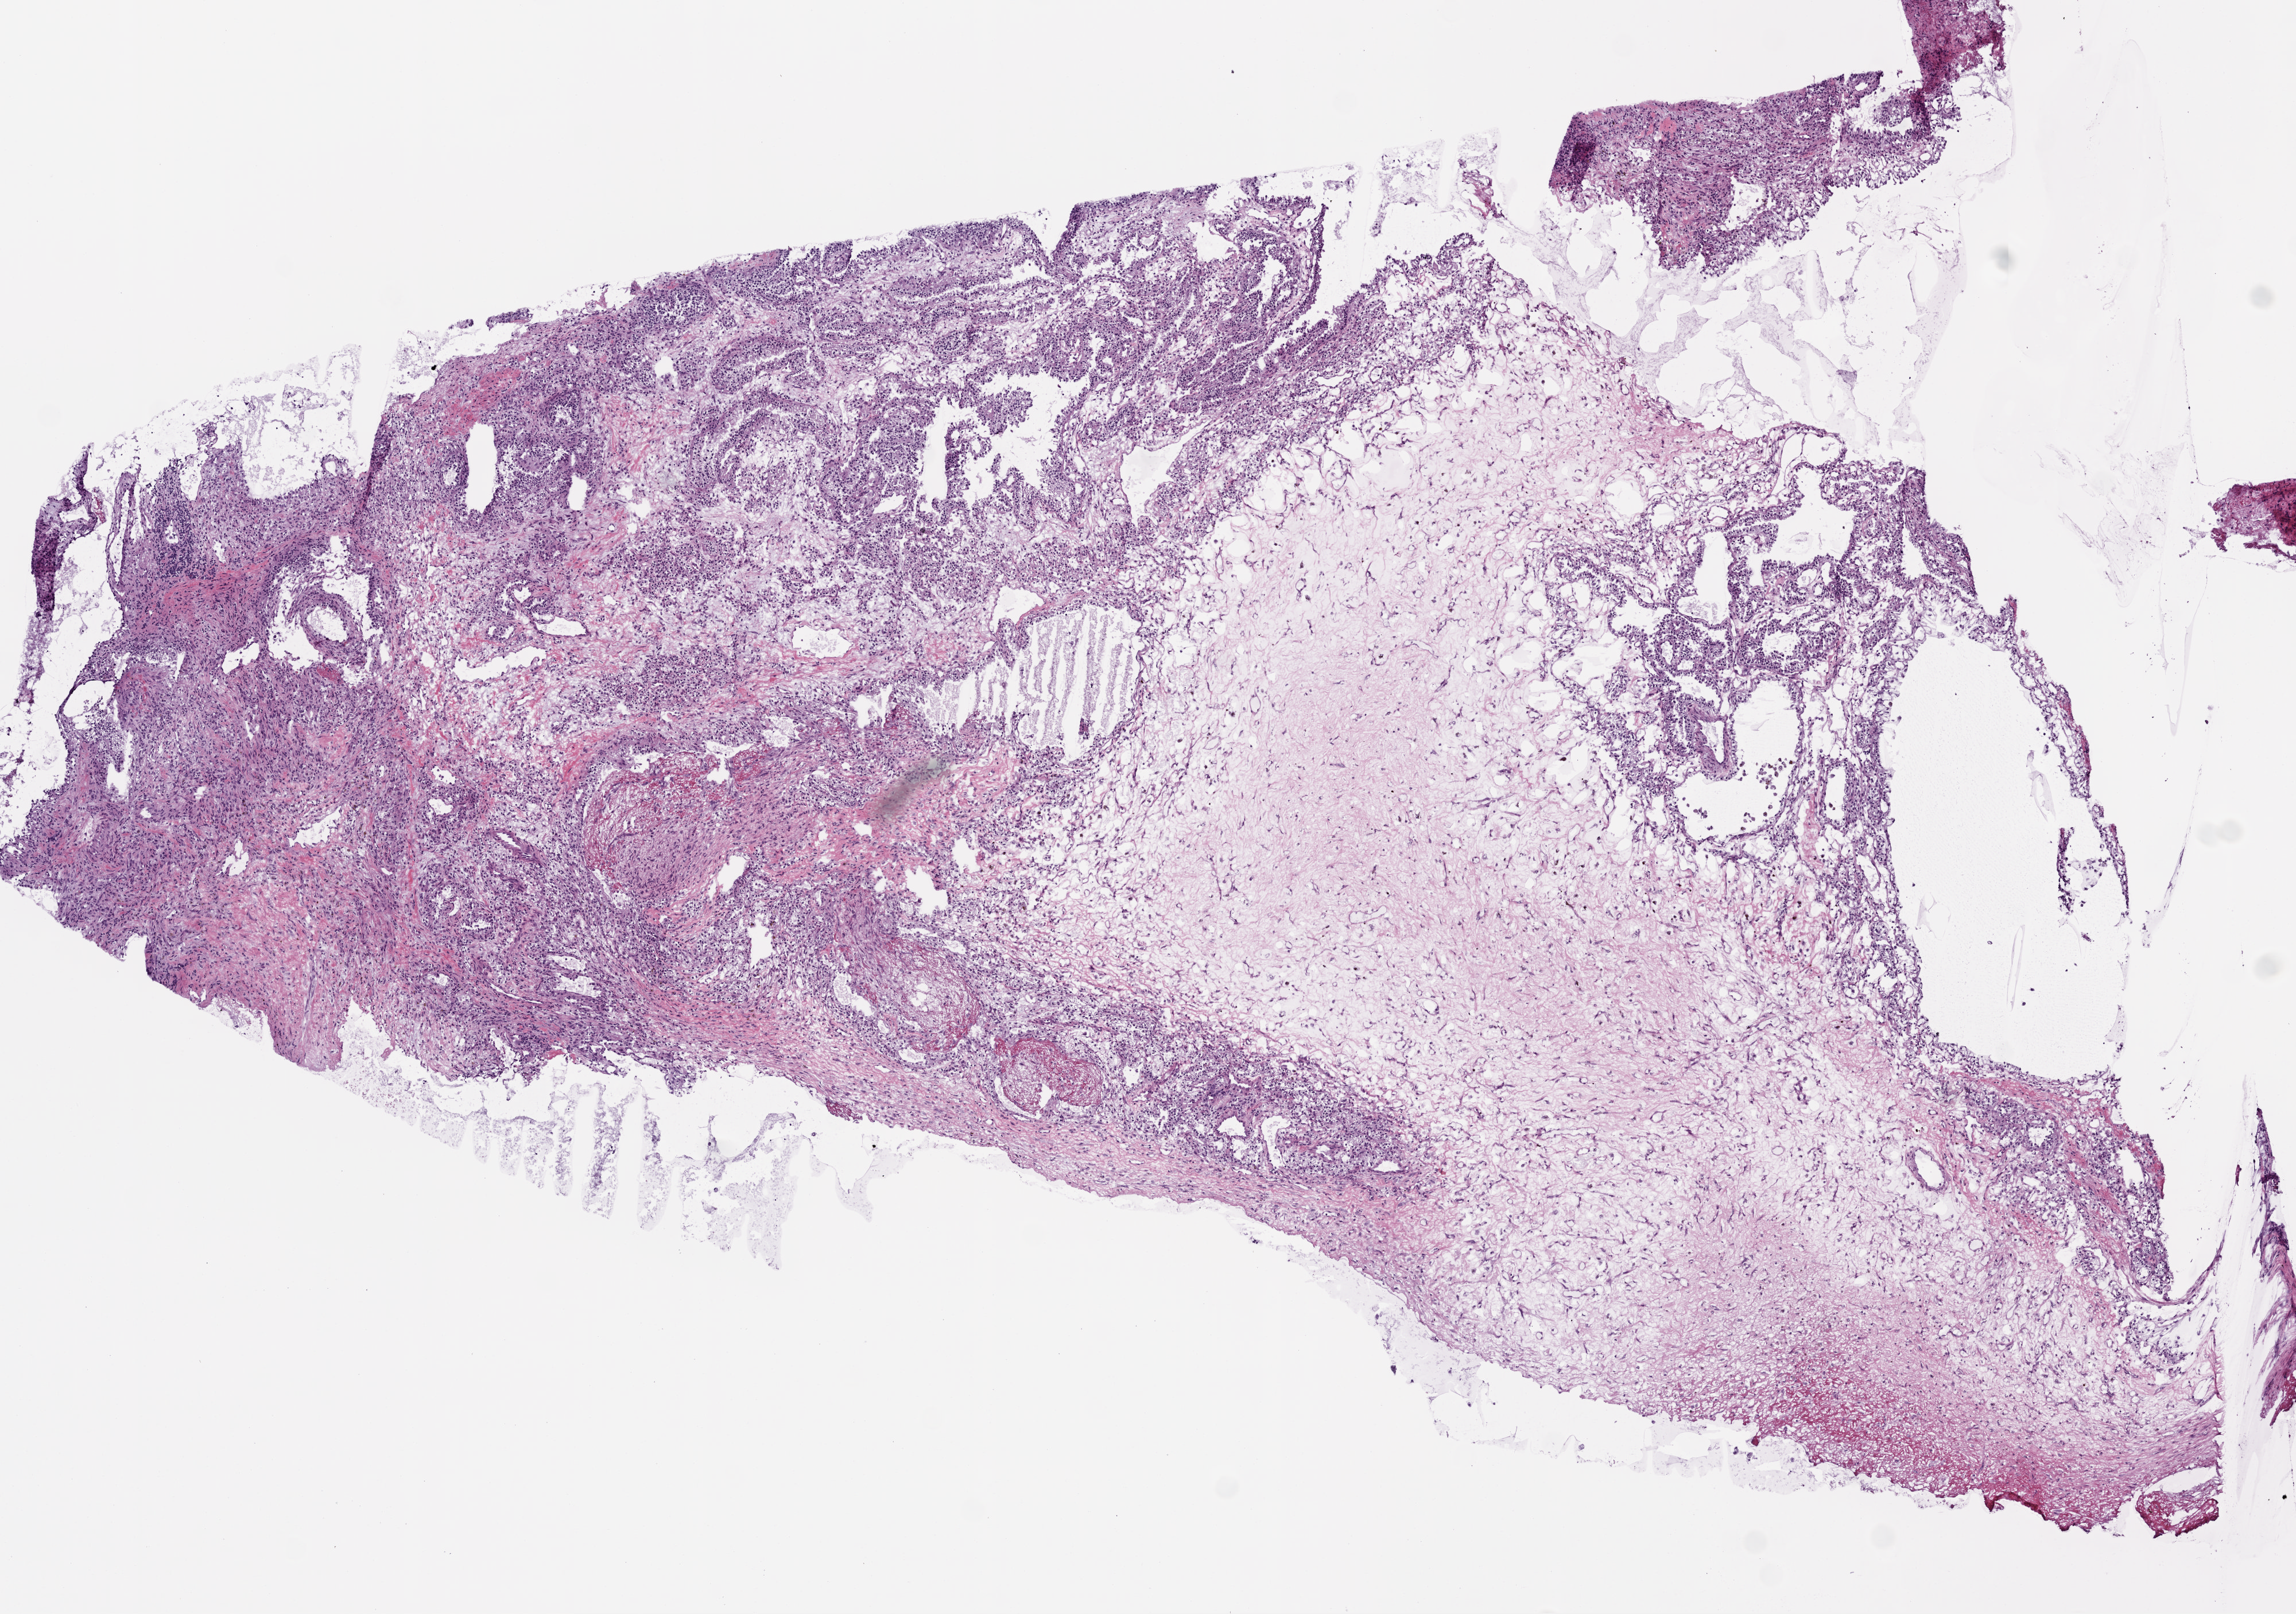
H&E-stained whole-slide image, whole scanned area (about 8.0 x 5.6 mm, from a 20x scan) shown as a low-resolution overview; frozen section from the top of the tissue portion; sample: primary tumour, kidney. Male patient; age at initial diagnosis 42 years. Histologic grade: G2 (moderately differentiated). Slide review estimates, as recorded: tumour cells 50%, tumour nuclei 80%, normal cells 0%, stromal cells 50%, necrosis 0%.
AJCC pathologic stage: I (7th edition). Histologic diagnosis: Clear cell adenocarcinoma, NOS. Laterality: left.